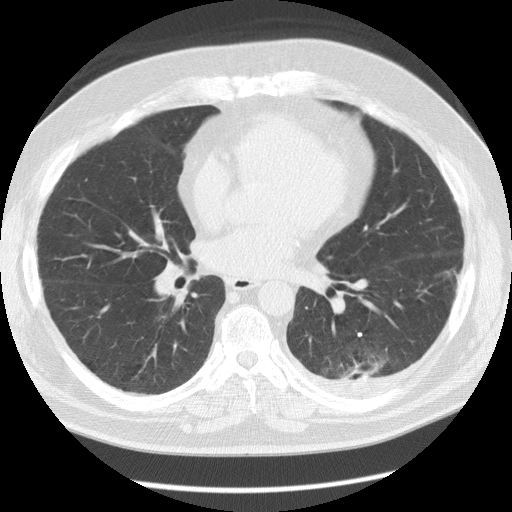
Axial slice from a low-dose chest CT screening exam. Baseline annual screen. Lung window (W 1500 / L -600 HU). Male, age 56 years at enrolment.
- Expert-annotated lung lesion, box from (x=325, y=345) to (x=399, y=398) px.
- The screening reader recorded 4 non-calcified nodules or masses ≥4 mm on this exam; which of them this box marks is not recorded.
- Official screen result: positive, change unspecified: nodule(s) >= 4 mm or enlarging nodule(s), mass(es), or other non-specific abnormalities suspicious for lung cancer.
- Participant outcome: lung cancer diagnosed 173 days after this screen — non-small cell carcinoma, left lower lobe, stage IV (AJCC 6th edition), 50 mm at pathology.